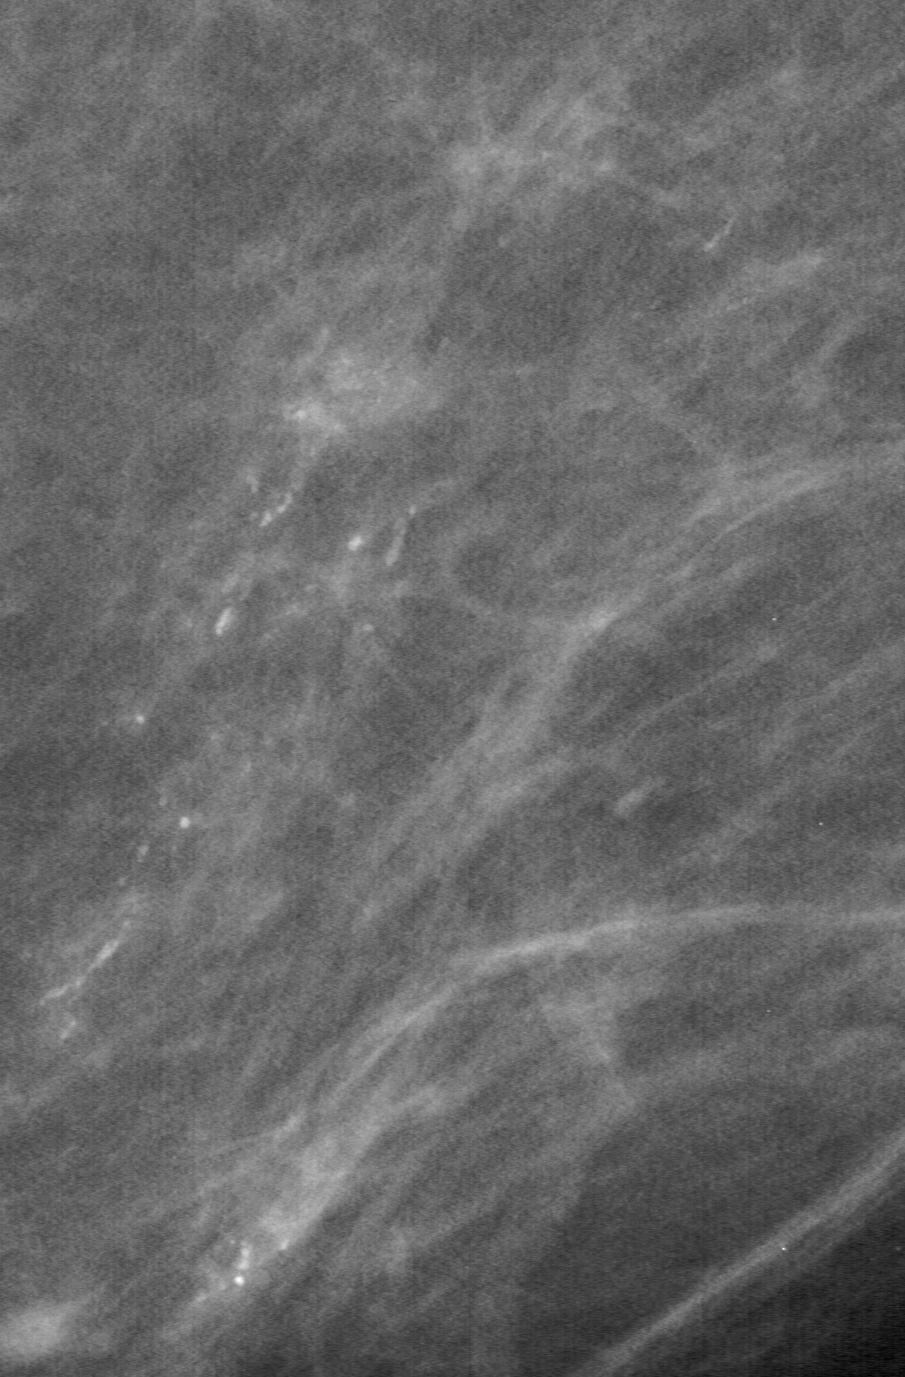
Cropped region of a digitized screen-film mammogram centred on a radiologist-marked abnormality, left breast, MLO view.
- Finding: calcifications, morphology fine linear branching, distribution segmental; BI-RADS assessment category 5; pathology result (as recorded, not read from the image): malignant.